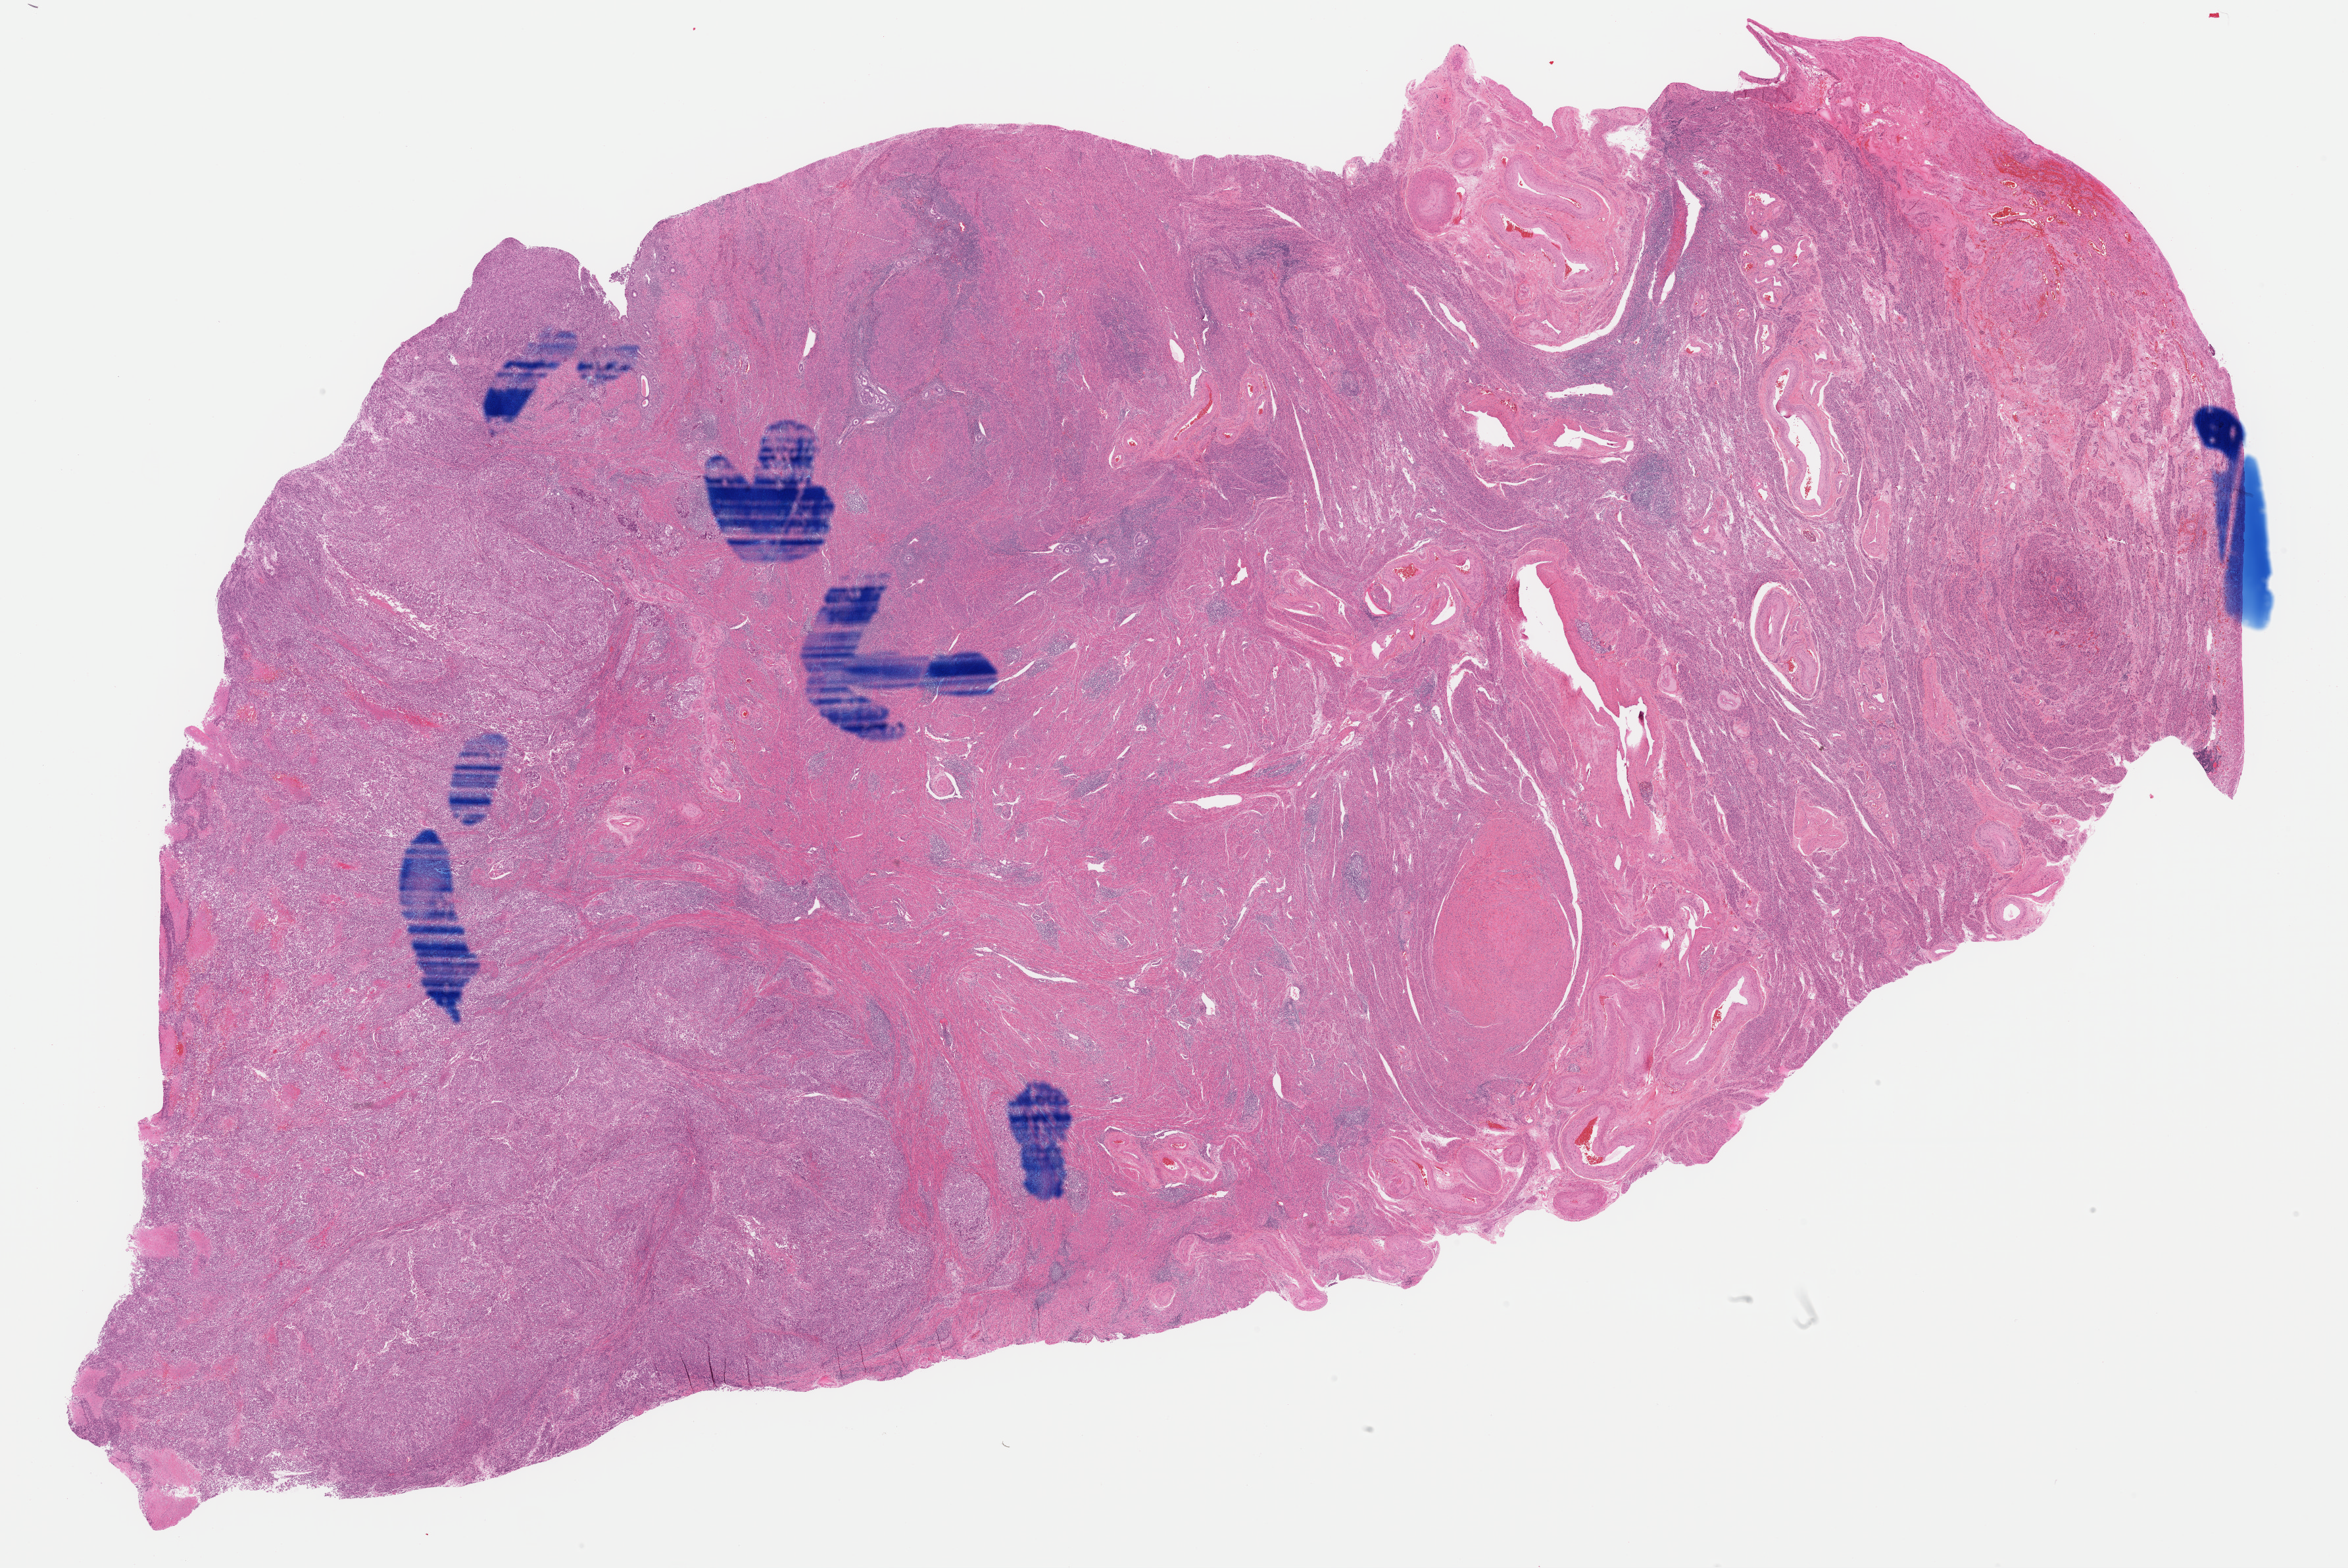
H&E whole-slide image, a low-resolution overview of the entire scanned area, about 28.2 x 18.8 mm (acquisition: 40x scan), formalin-fixed paraffin-embedded (FFPE) diagnostic section, primary tumour sample from the uterus. Female patient; age at initial diagnosis 68 years. Histologic grade: G3 (poorly differentiated).
Histologic diagnosis: Serous cystadenocarcinoma, NOS (endometrium). FIGO stage: IA.